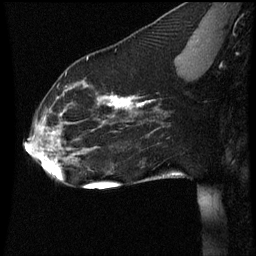
Breast MRI (dynamic contrast-enhanced), one sagittal slice; slice 22 of 60 in the series (ordered by position); dynamic contrast-enhanced series, image 2 of 3 at this slice position (ordered by acquisition); 1.5 T; TE 4.2 ms, TR 8.9 ms; 2 mm slice thickness; 256 × 256 image matrix, field of view 200 × 200 mm. Patient: female, 35 years. From the clinical record (not read from this slice): setting: breast cancer imaged before/during neoadjuvant chemotherapy; receptor status: HER2-positive.
Outlined on this slice (semi-automatic segmentation, software-assisted and operator-edited):
- analysis volume of interest (the breast-tissue region the enhancement analysis was run in; not a lesion): bounding box (x1, y1, x2, y2) in pixels: (23, 66, 177, 177)
- tumour enhancement mask (voxels above the 70 % enhancement threshold inside the analysis volume of interest): (41, 94, 150, 155)